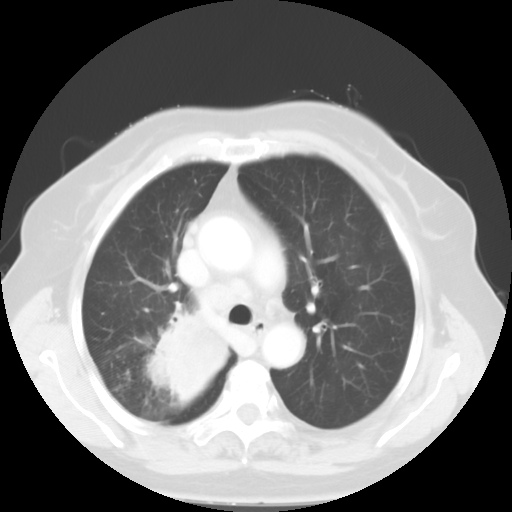
Chest CT, one axial slice. Slice 36 of 52 in the series (ordered by position). Reconstruction kernel STANDARD. 120 kVp. Lung window (W 1500 / L -600 HU). 512 × 512 image matrix, field of view 333 × 333 mm. Female patient, age 81 years. Case-level facts recorded for this patient, not image findings: clinical TNM (as recorded): T4 N3 M1b.
Annotated regions visible in this slice (bounding box drawn by a radiologist):
- lung tumour (recorded histology: adenocarcinoma): box from (x=147, y=309) to (x=230, y=400) px